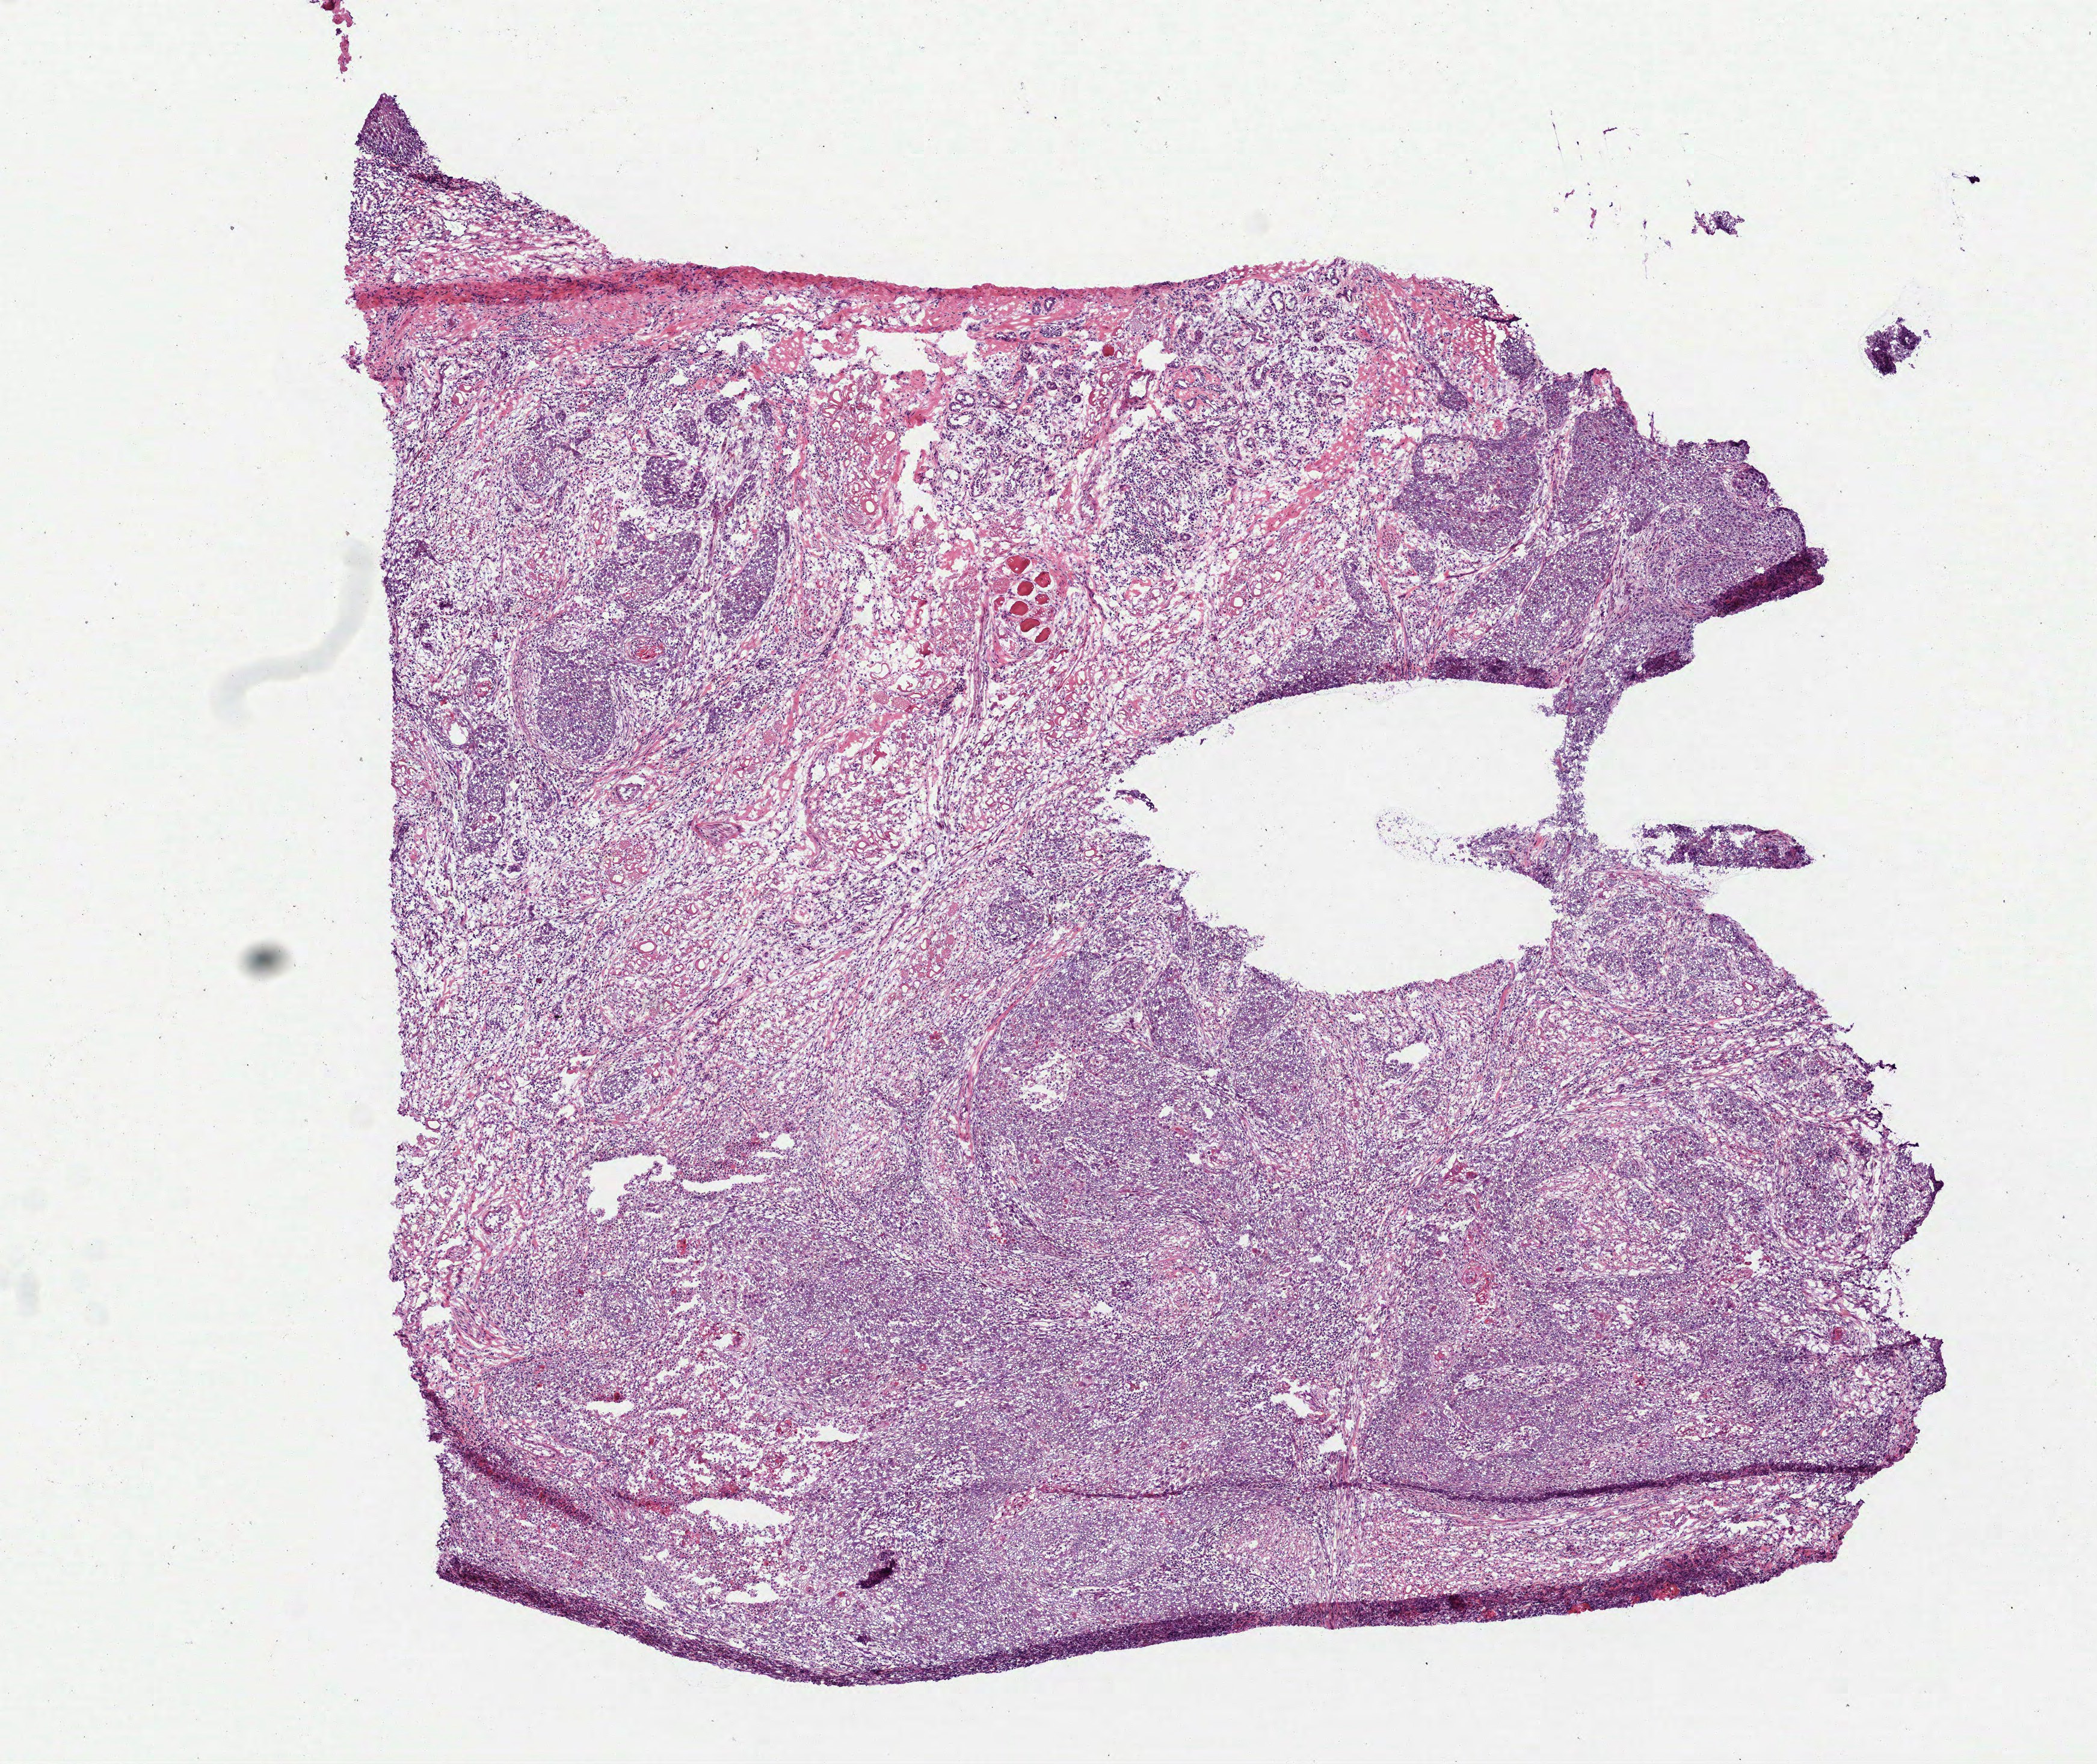
Whole-slide histology image, H&E, shown as a low-resolution overview of the whole scanned area (about 7.0 x 5.9 mm), frozen section from the bottom of the tissue portion, head and neck, primary tumour sample. Patient: female, age at initial diagnosis 50 years. Histologic grade: G2 (moderately differentiated). Slide review estimates, as recorded: tumour cells 74%, tumour nuclei 60%, normal cells 0%, stromal cells 25%, necrosis 1%.
* TNM: T3 N2a
* laterality: right
* AJCC pathologic stage: IVA
* diagnosis: Squamous cell carcinoma, NOS (tongue, NOS)